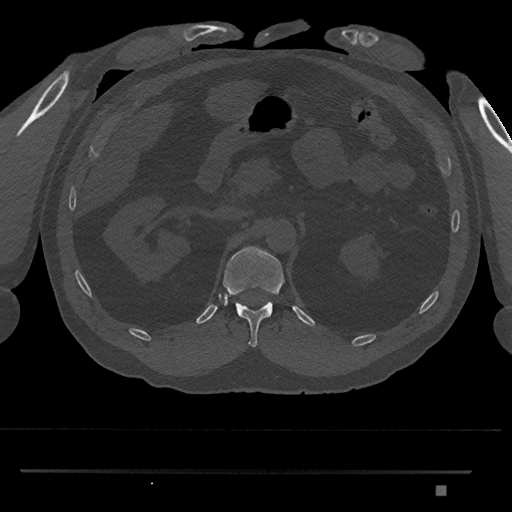
CT including the spine, one axial slice; slice 876 of 1134 in the series (ordered by position); reconstruction kernel Br40s/3; bone window (W 1800 / L 400 HU); 0.5 mm slice thickness; 512 × 512 image matrix. Patient: male, 65 years. Case-level facts recorded for this patient, not image findings: primary cancer: prostate.
Annotated regions visible in this slice (semi-automatic segmentation, software-assisted and operator-edited):
- T12 vertebra: bounding box (x1, y1, x2, y2) in pixels: (222, 246, 285, 347)